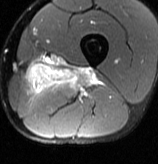
MRI of an extremity soft-tissue mass, one axial slice. Position 24 of 70 along the scan axis. T2-weighted fat-saturated. MR volume resampled by the dataset authors to the PET/CT grid (not the native acquisition matrix). 158 × 164 image matrix, field of view 154 × 160 mm. Male patient. Case-level facts recorded for this patient, not image findings: histological type: extraskeletal osteosarcoma; grade: high; site of the primary tumour: left adductur.
Outlined on this slice (expert contour drawn on MRI and transferred to this co-registered scan by the dataset authors):
- gross tumour volume (mass): bounding box (x1, y1, x2, y2) in pixels: (24, 62, 100, 93)